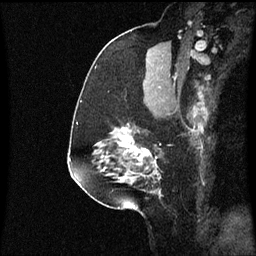
Breast MRI (dynamic contrast-enhanced), one sagittal slice; slice 38 of 60 in the series (ordered by position); dynamic contrast-enhanced series, image 2 of 3 at this slice position (ordered by acquisition); 1.5 T; TE 4.2 ms, TR 8.9 ms; 2 mm slice thickness; 256 × 256 image matrix, field of view 200 × 200 mm. Patient: female, 58 years. From the clinical record (not read from this slice): setting: breast cancer imaged before/during neoadjuvant chemotherapy; receptor status: triple-negative.
Outlined on this slice (semi-automatic segmentation, software-assisted and operator-edited):
- analysis volume of interest (the breast-tissue region the enhancement analysis was run in; not a lesion): box from (x=104, y=124) to (x=163, y=179) px
- tumour enhancement mask (voxels above the 70 % enhancement threshold inside the analysis volume of interest): (x=104, y=128)–(x=157, y=179)